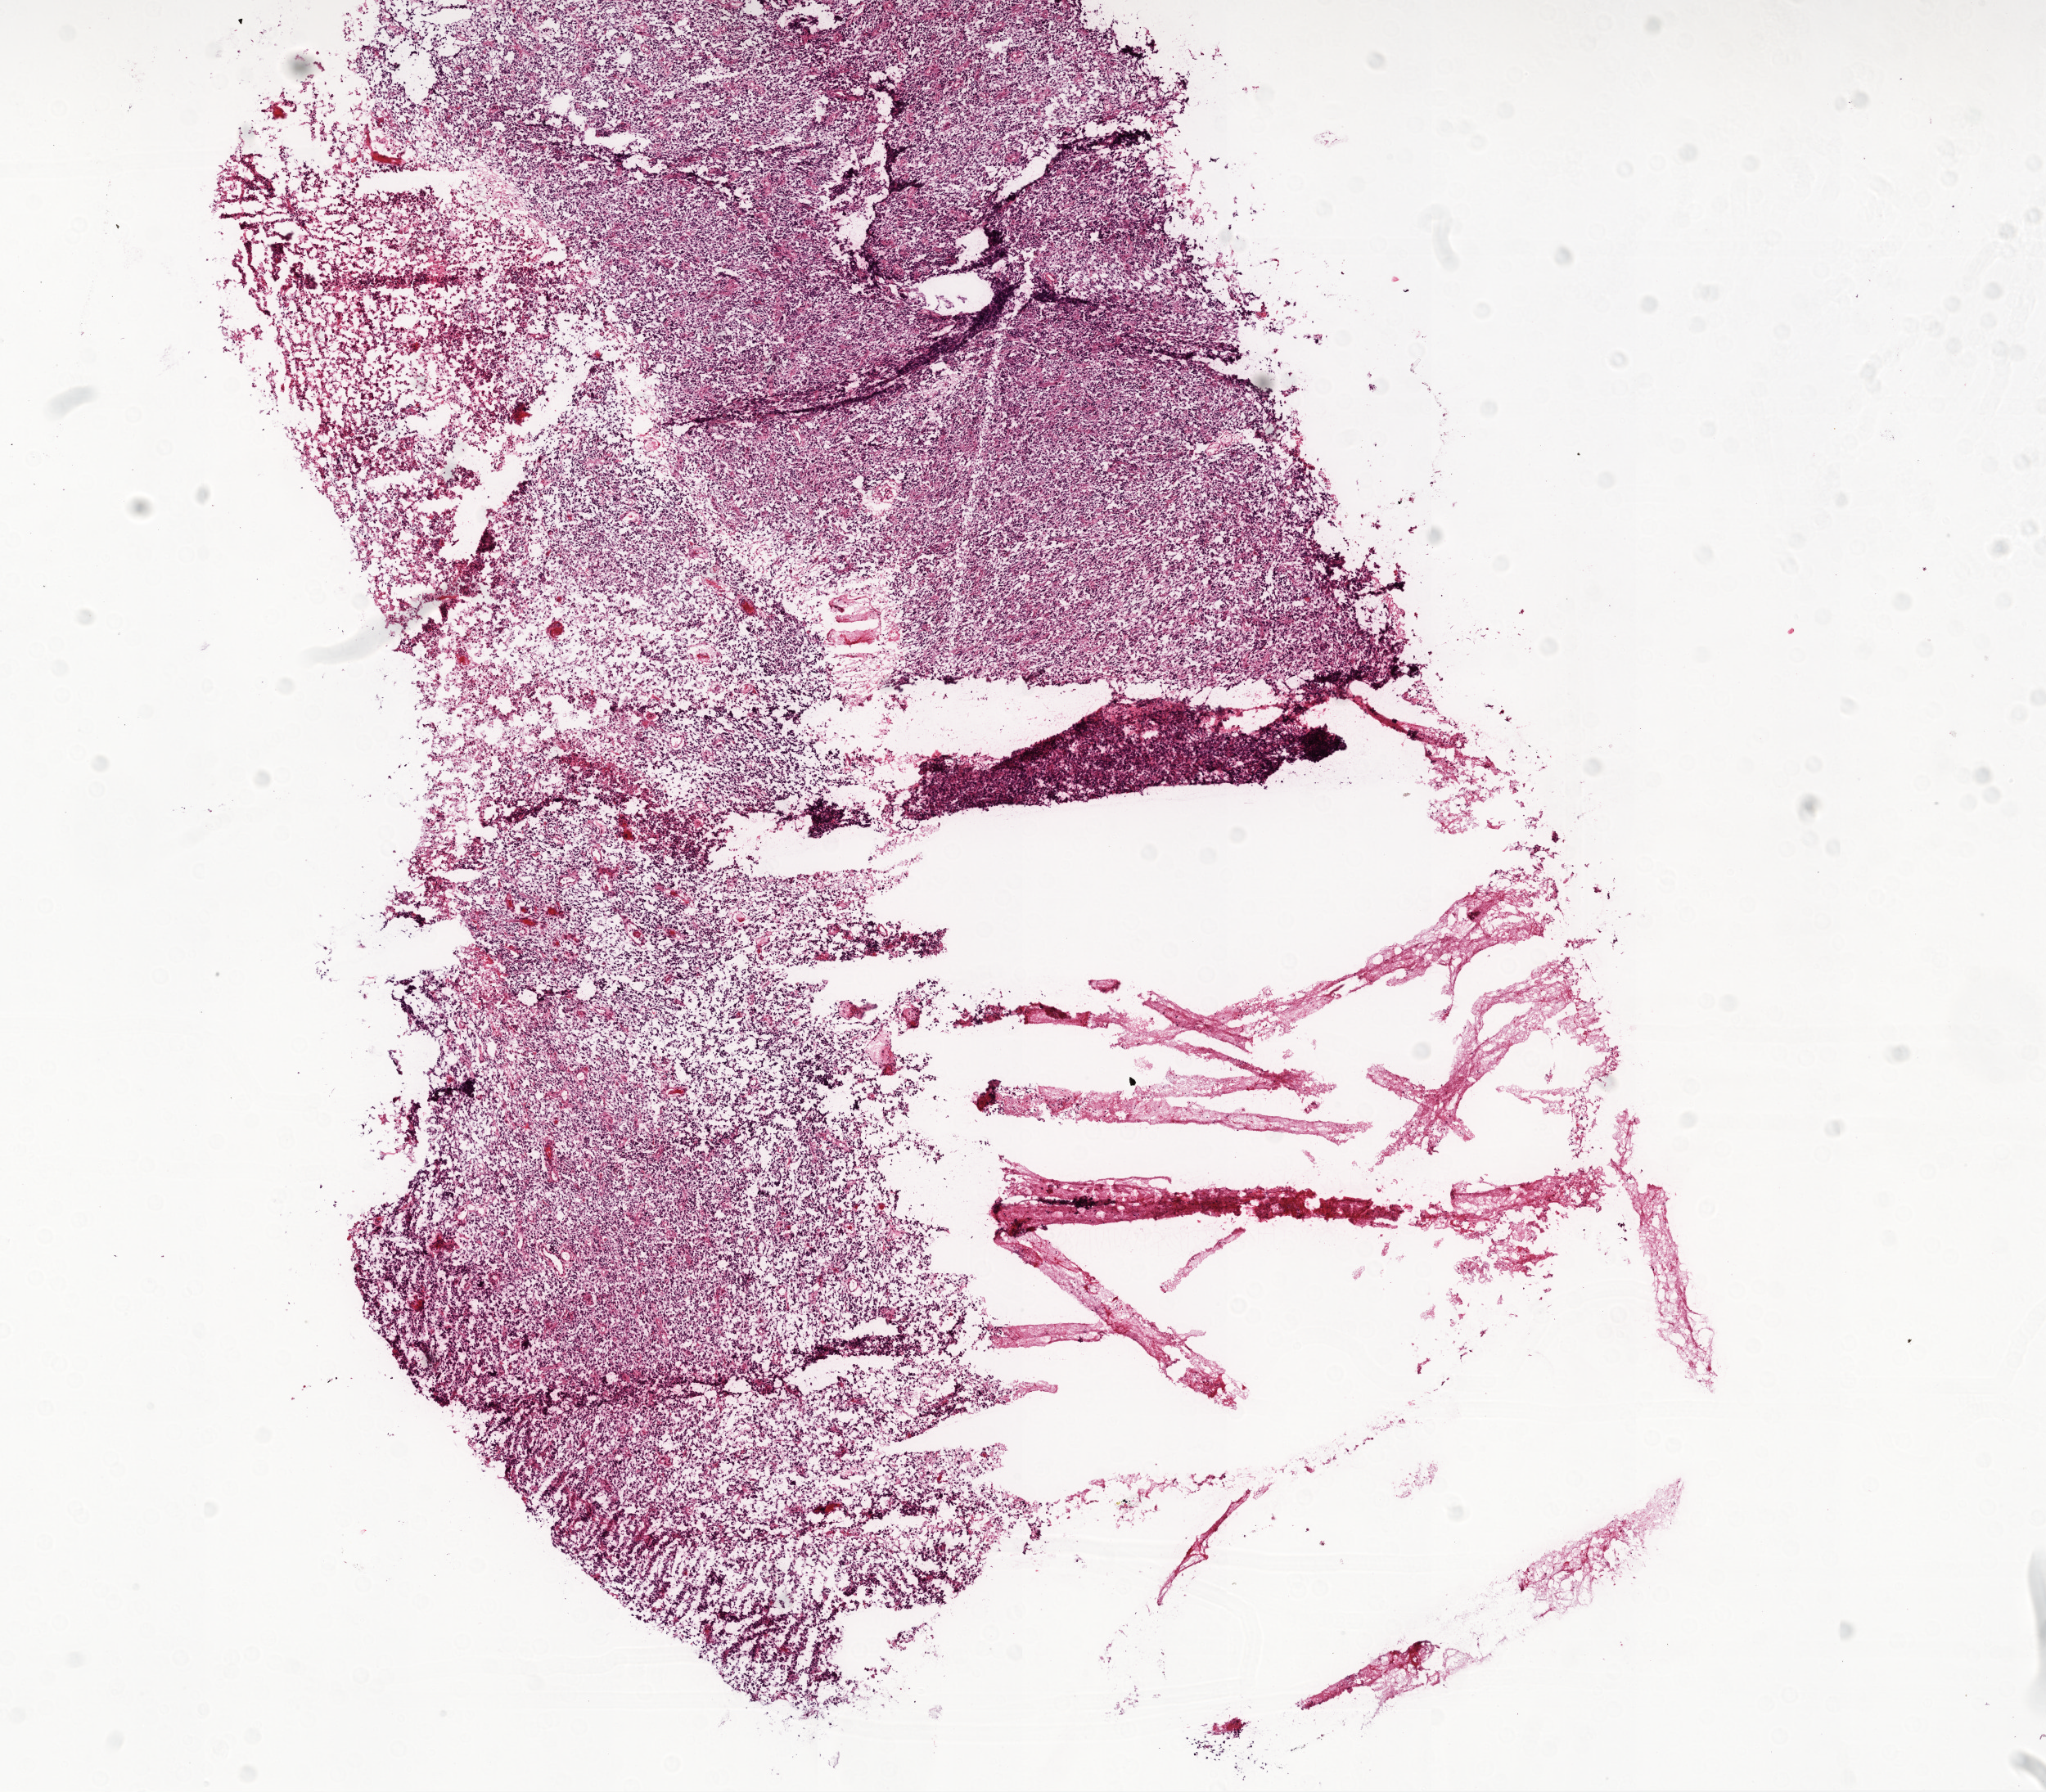
H&E whole-slide image — whole scanned area (about 10.0 x 8.8 mm, slide scanned at 20x) shown as a low-resolution overview; frozen section from the top of the tissue portion; sample: primary tumour, brain. Patient: male, age at initial diagnosis 67 years. Slide review estimates, as recorded: tumour cells 95%, tumour nuclei 100%, normal cells 0%, stromal cells 0%, necrosis 5%.
Histologic diagnosis: Glioblastoma.